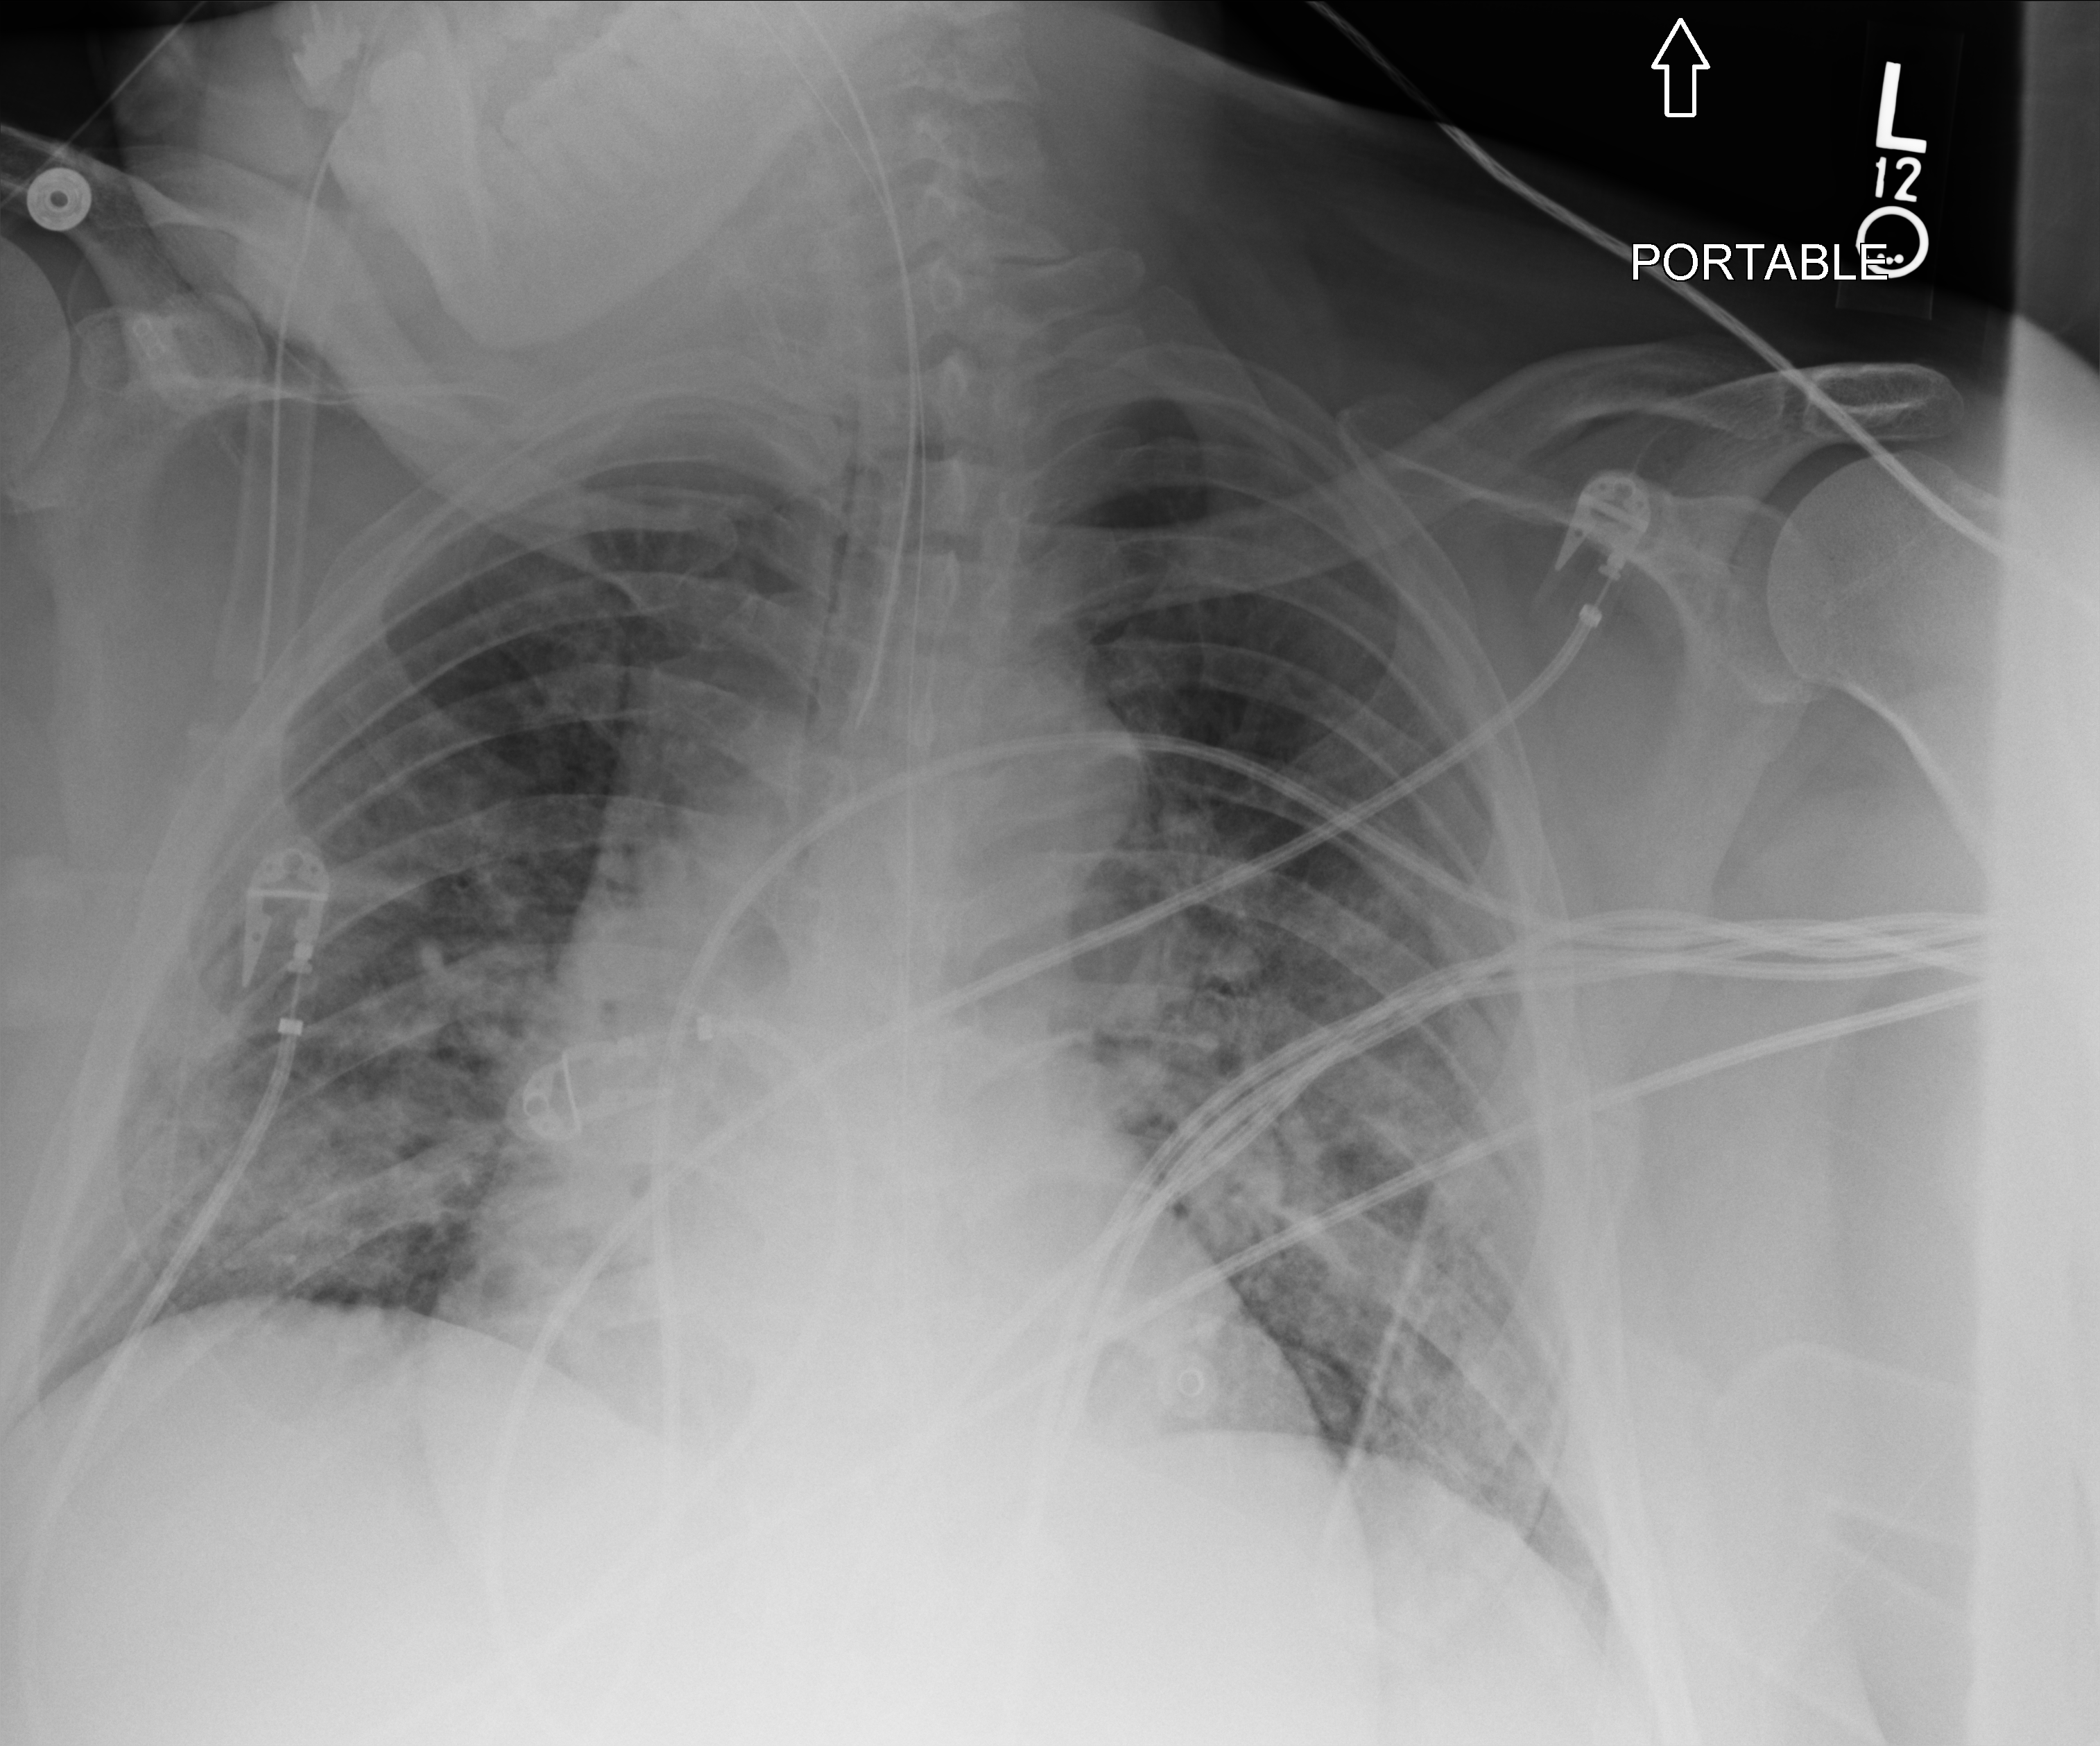
Portable chest radiograph, anteroposterior (AP) projection. Male patient hospitalised with COVID-19, age 60–74 years.
From the hospital-stay record, not from the radiograph (when in the stay this image was taken is not recorded): other chronic lung disease (admission record): no; admitted to intensive care during this hospital stay: yes; mechanically ventilated during this hospital stay: yes.